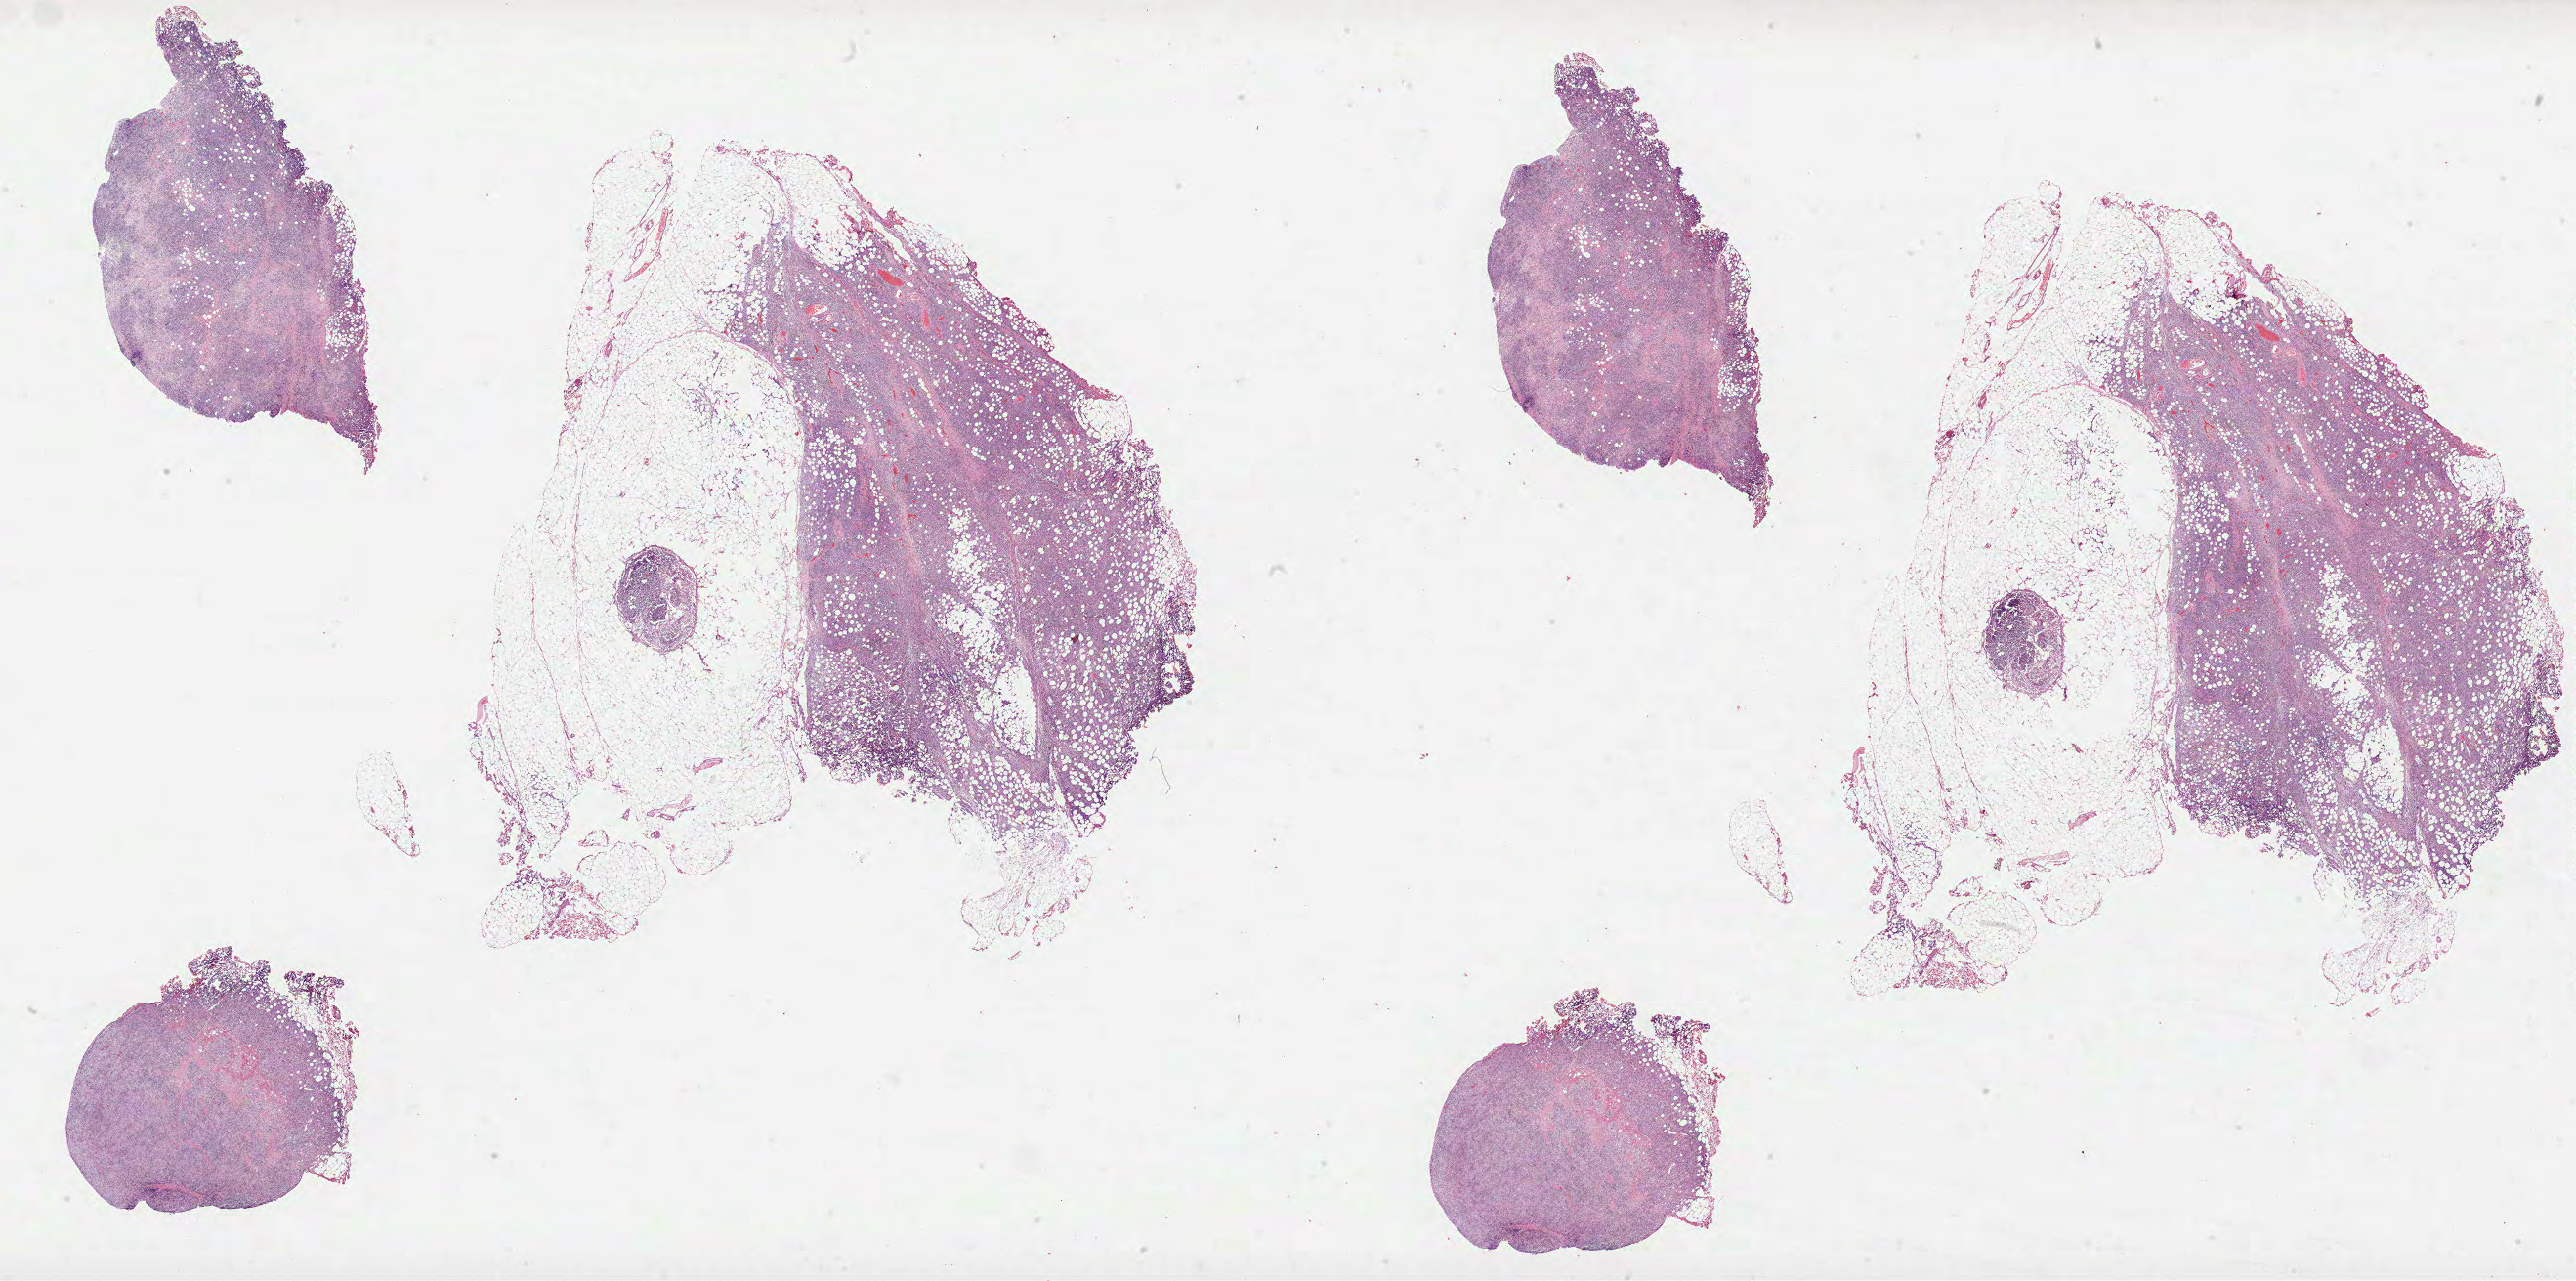
Whole-slide histology image, H&E-stained, whole scanned area (about 42.5 x 21.2 mm) shown as a low-resolution overview, formalin-fixed paraffin-embedded (FFPE) diagnostic section, lymphoid tissue, primary tumour sample. Patient: male, age at initial diagnosis 52 years.
Diagnosis: Diffuse large B-cell lymphoma, NOS (specified parts of peritoneum).